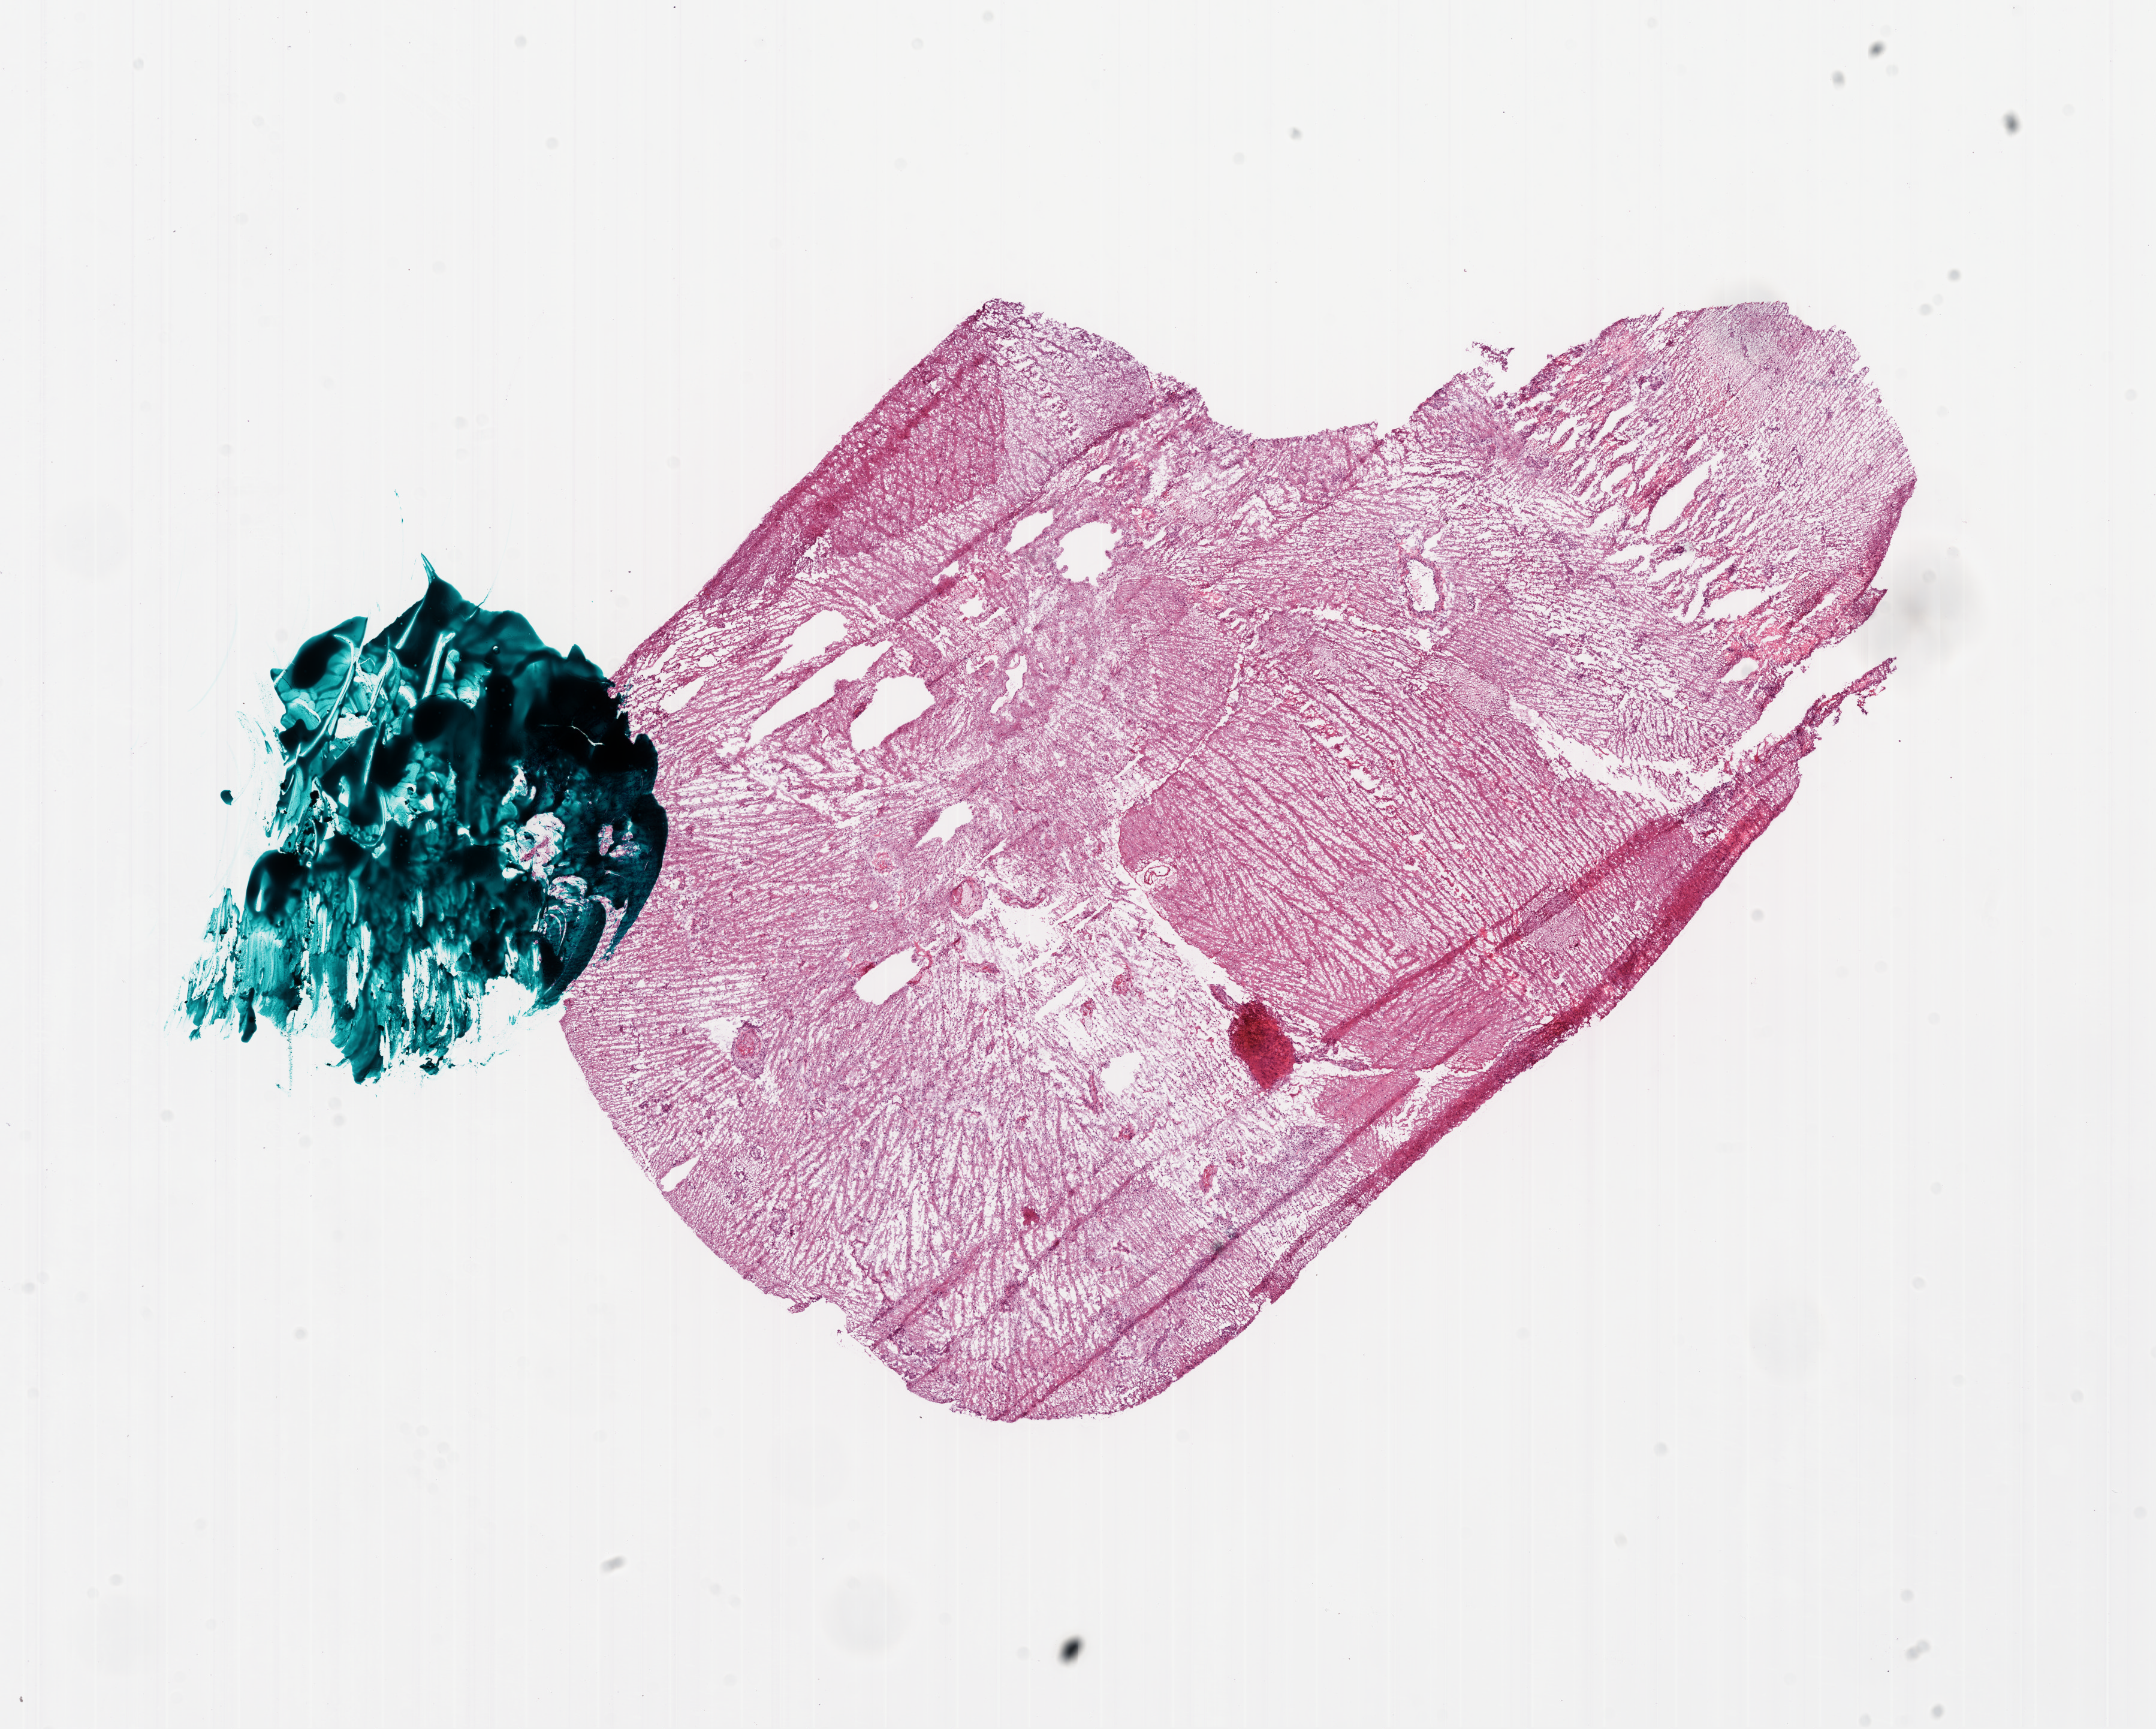
Digitized H&E-stained tissue section (whole slide) — a low-resolution overview of the entire scanned area, about 14.5 x 11.6 mm (slide scanned at 20x); frozen section; brain, primary tumour sample. Female patient; age at initial diagnosis 39 years. Pathologist review of this section (percent, as recorded): tumour cells 0%, tumour nuclei 50%, normal cells 0%, stromal cells 100%, necrosis 0%.
- diagnosis: Glioblastoma